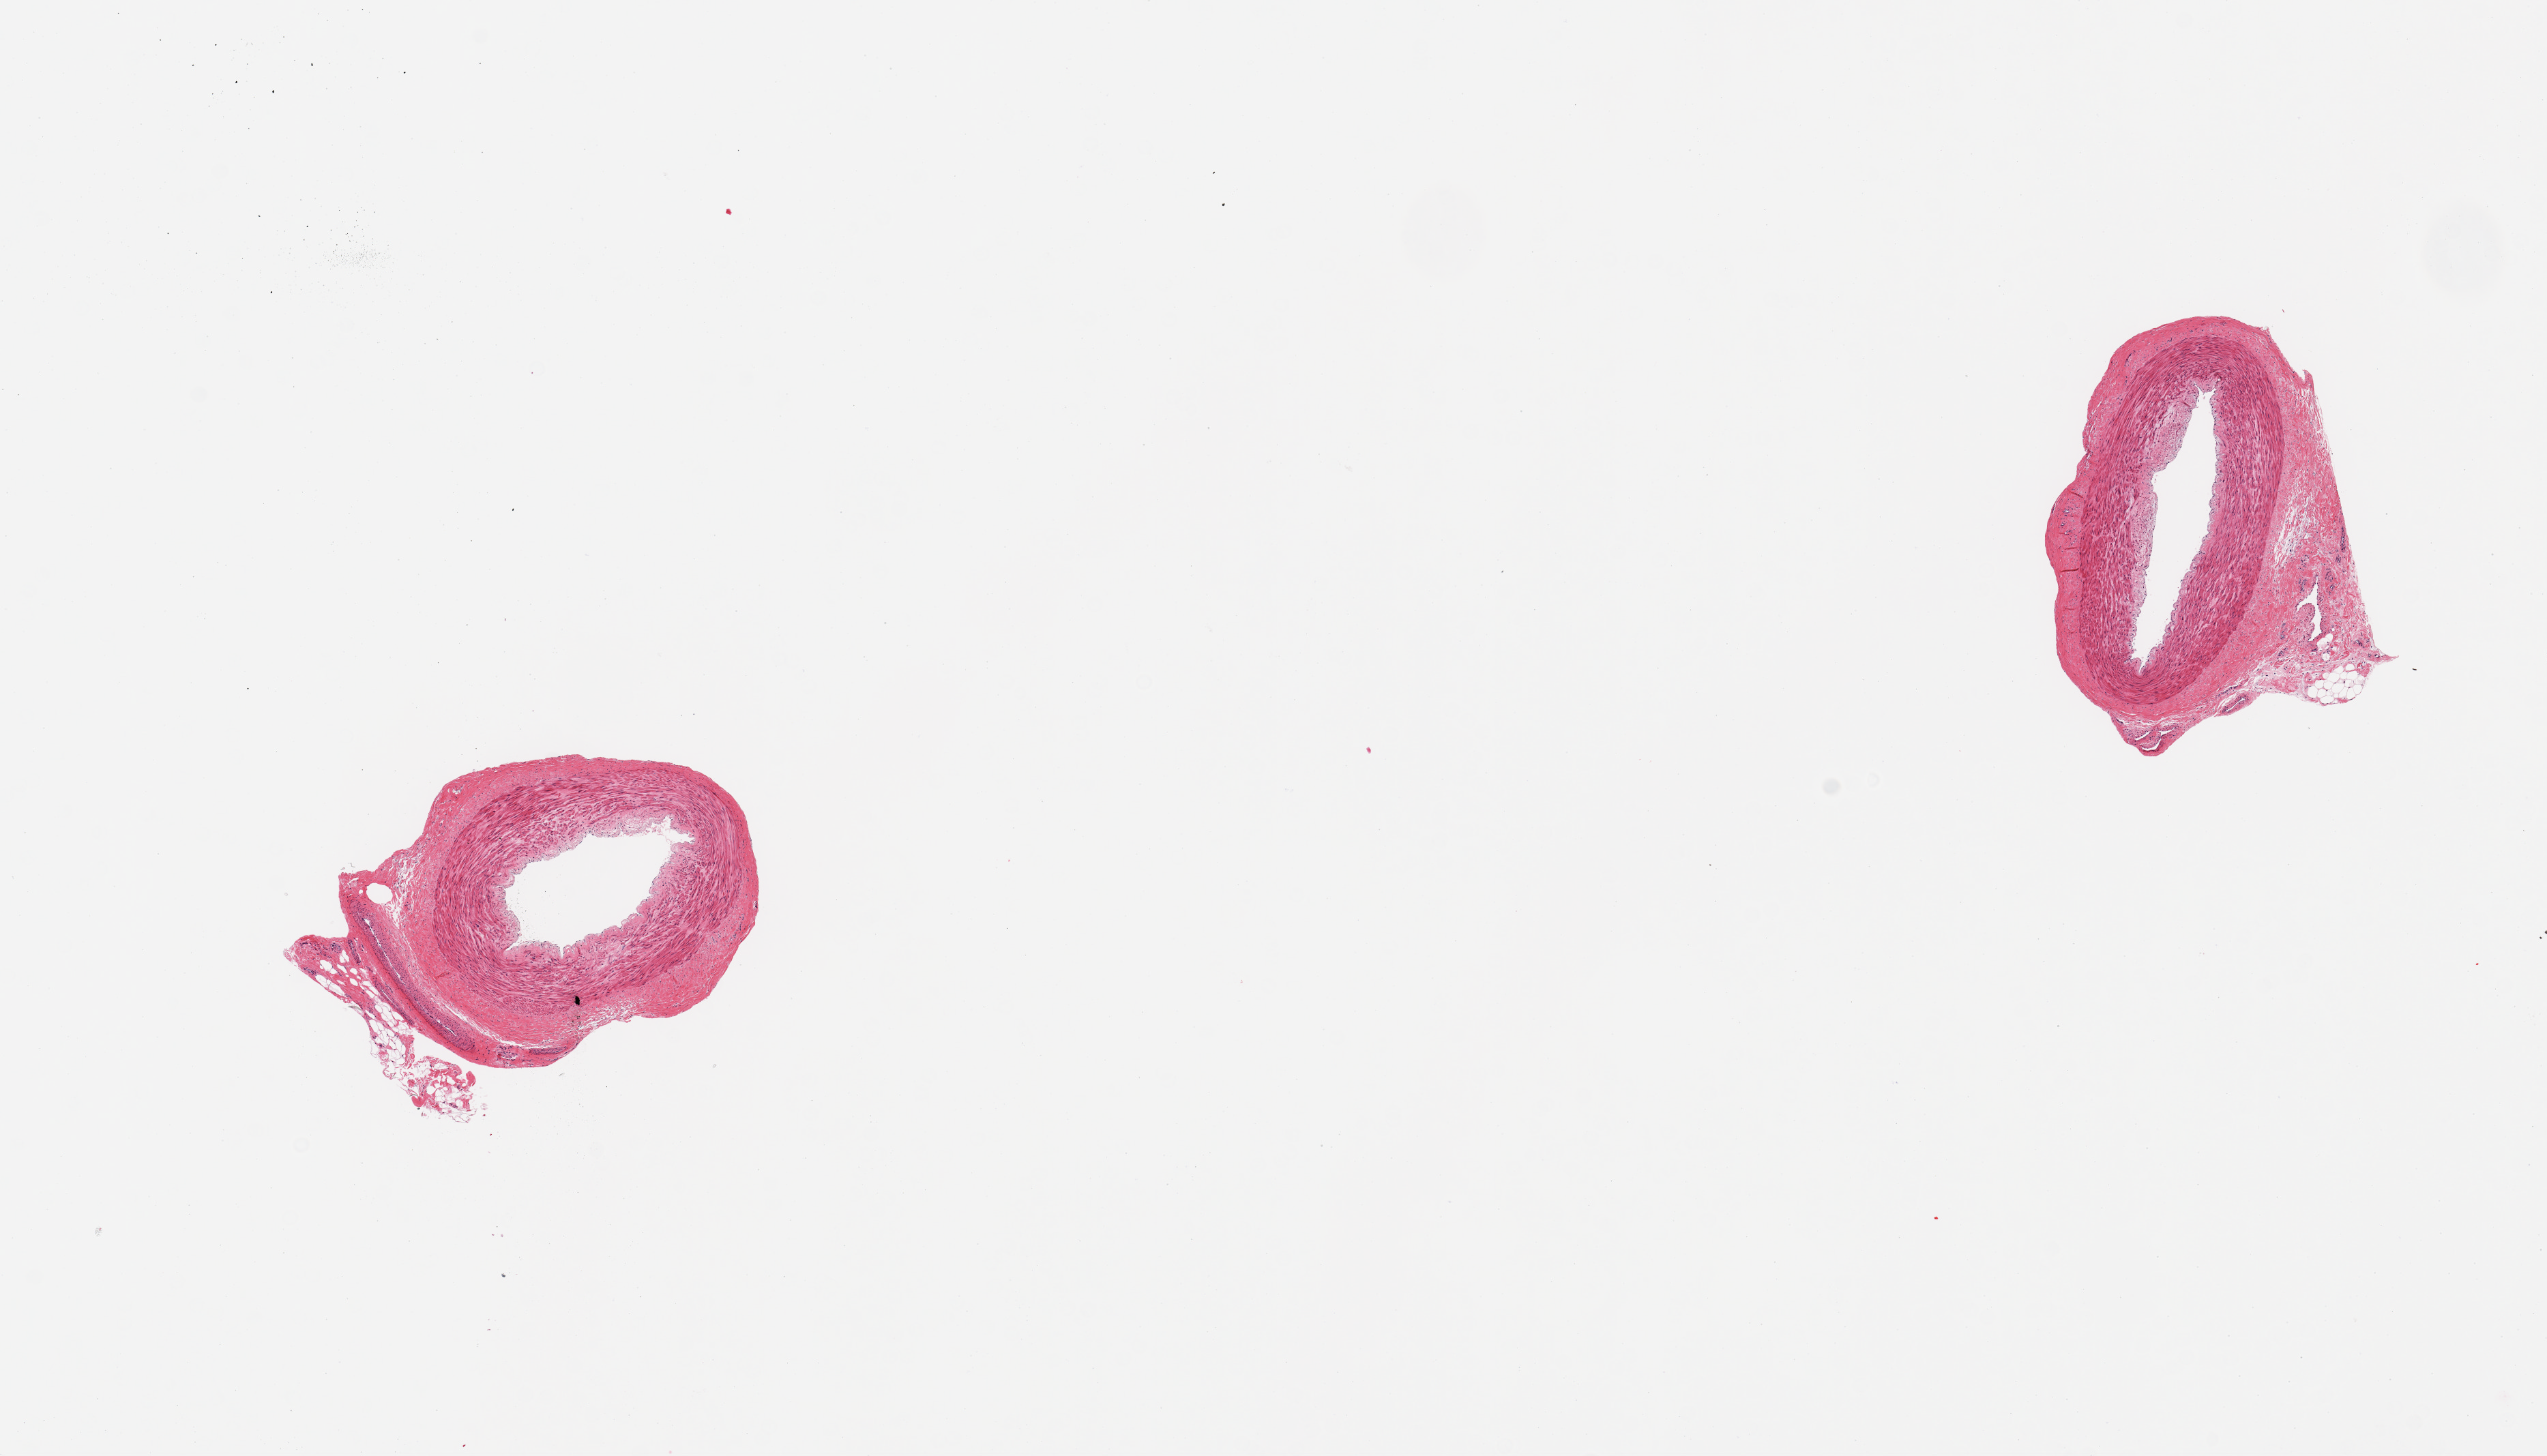
Digitized H&E-stained section, brightfield, whole scanned area (about 14.8 x 8.4 mm) shown as a low-resolution overview. PAXgene-fixed, paraffin-embedded tissue. Sampled site (target tissue): tibial artery. Tissue donor sample. Donor sex: male.
Pathologist's review note for this sample: 2 pieces; essentially well trimmed.